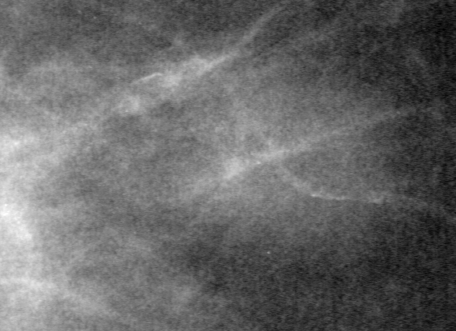
Region of interest cut from a scanned film mammogram (one marked finding), right breast, CC view.
Marked abnormality: mass, shape oval, margins ill defined; BI-RADS assessment category 4; pathology result (as recorded, not read from the image): benign.